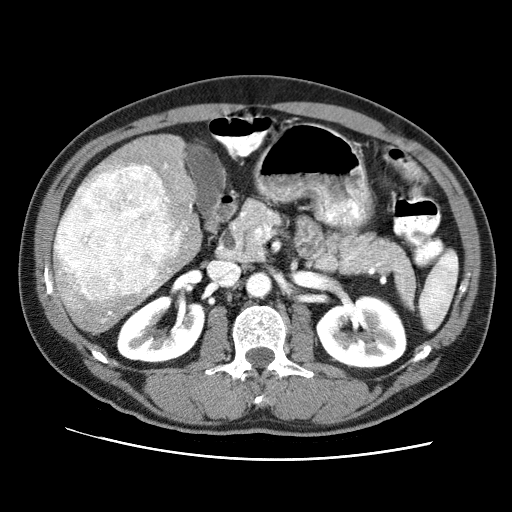
Contrast-enhanced abdominal CT (liver protocol), one axial slice. Position 35 of 71 along the scan axis. Reconstruction kernel STANDARD. Soft-tissue window (W 400 / L 40 HU). 2.5 mm slice thickness. 512 × 512 image matrix, field of view 360 × 360 mm. Case-level facts recorded for this patient, not image findings: diagnosis: hepatocellular carcinoma (patient treated with transarterial chemoembolisation; whether this scan precedes or follows treatment is not stated here); TNM stage (as recorded): Stage-II; Child-Pugh class: A; tumour nodularity: multinodular; tumour size: 4.6 cm.
Annotated regions visible in this slice (semi-automatic segmentation, software-assisted and operator-edited):
- liver parenchyma outside the tumour (the mass and vessels are separate outlines, so this box may not span the whole liver): bounding box <56,133,202,330> (left, top, right, bottom; pixels)
- mass: <54,164,178,300>
- liver vessels: <59,163,192,323>